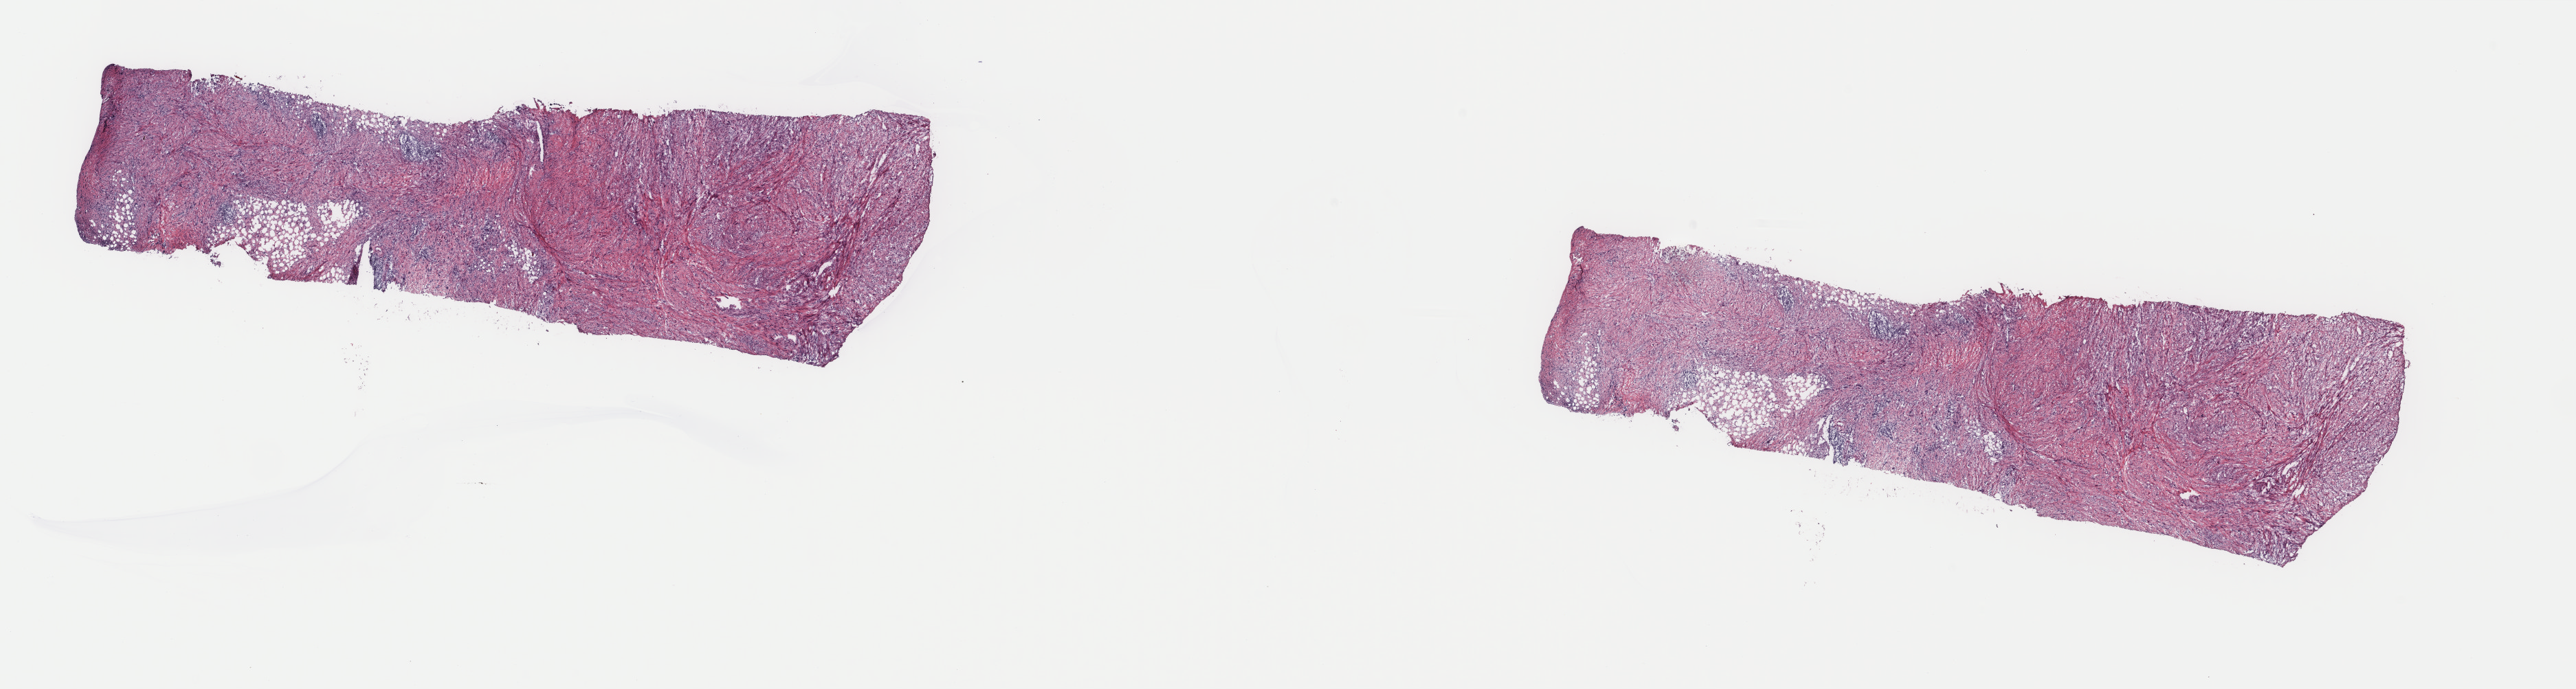
H&E-stained whole-slide image — low-resolution overview of the scanned area, about 29.7 x 8.0 mm (acquisition: 40x scan). Frozen section from the top of the tissue portion. Primary tumour sample from the retroperitoneum and peritoneum. Female, age 60 years at initial diagnosis. Pathologist review of this section (percent, as recorded): tumour cells 100%, tumour nuclei 80%, normal cells 0%, stromal cells 0%, necrosis 0%. Infiltration values recorded for this section: lymphocyte infiltration 3%, monocyte infiltration 0%, neutrophil infiltration 0%.
Pathologic diagnosis: Dedifferentiated liposarcoma (retroperitoneum).